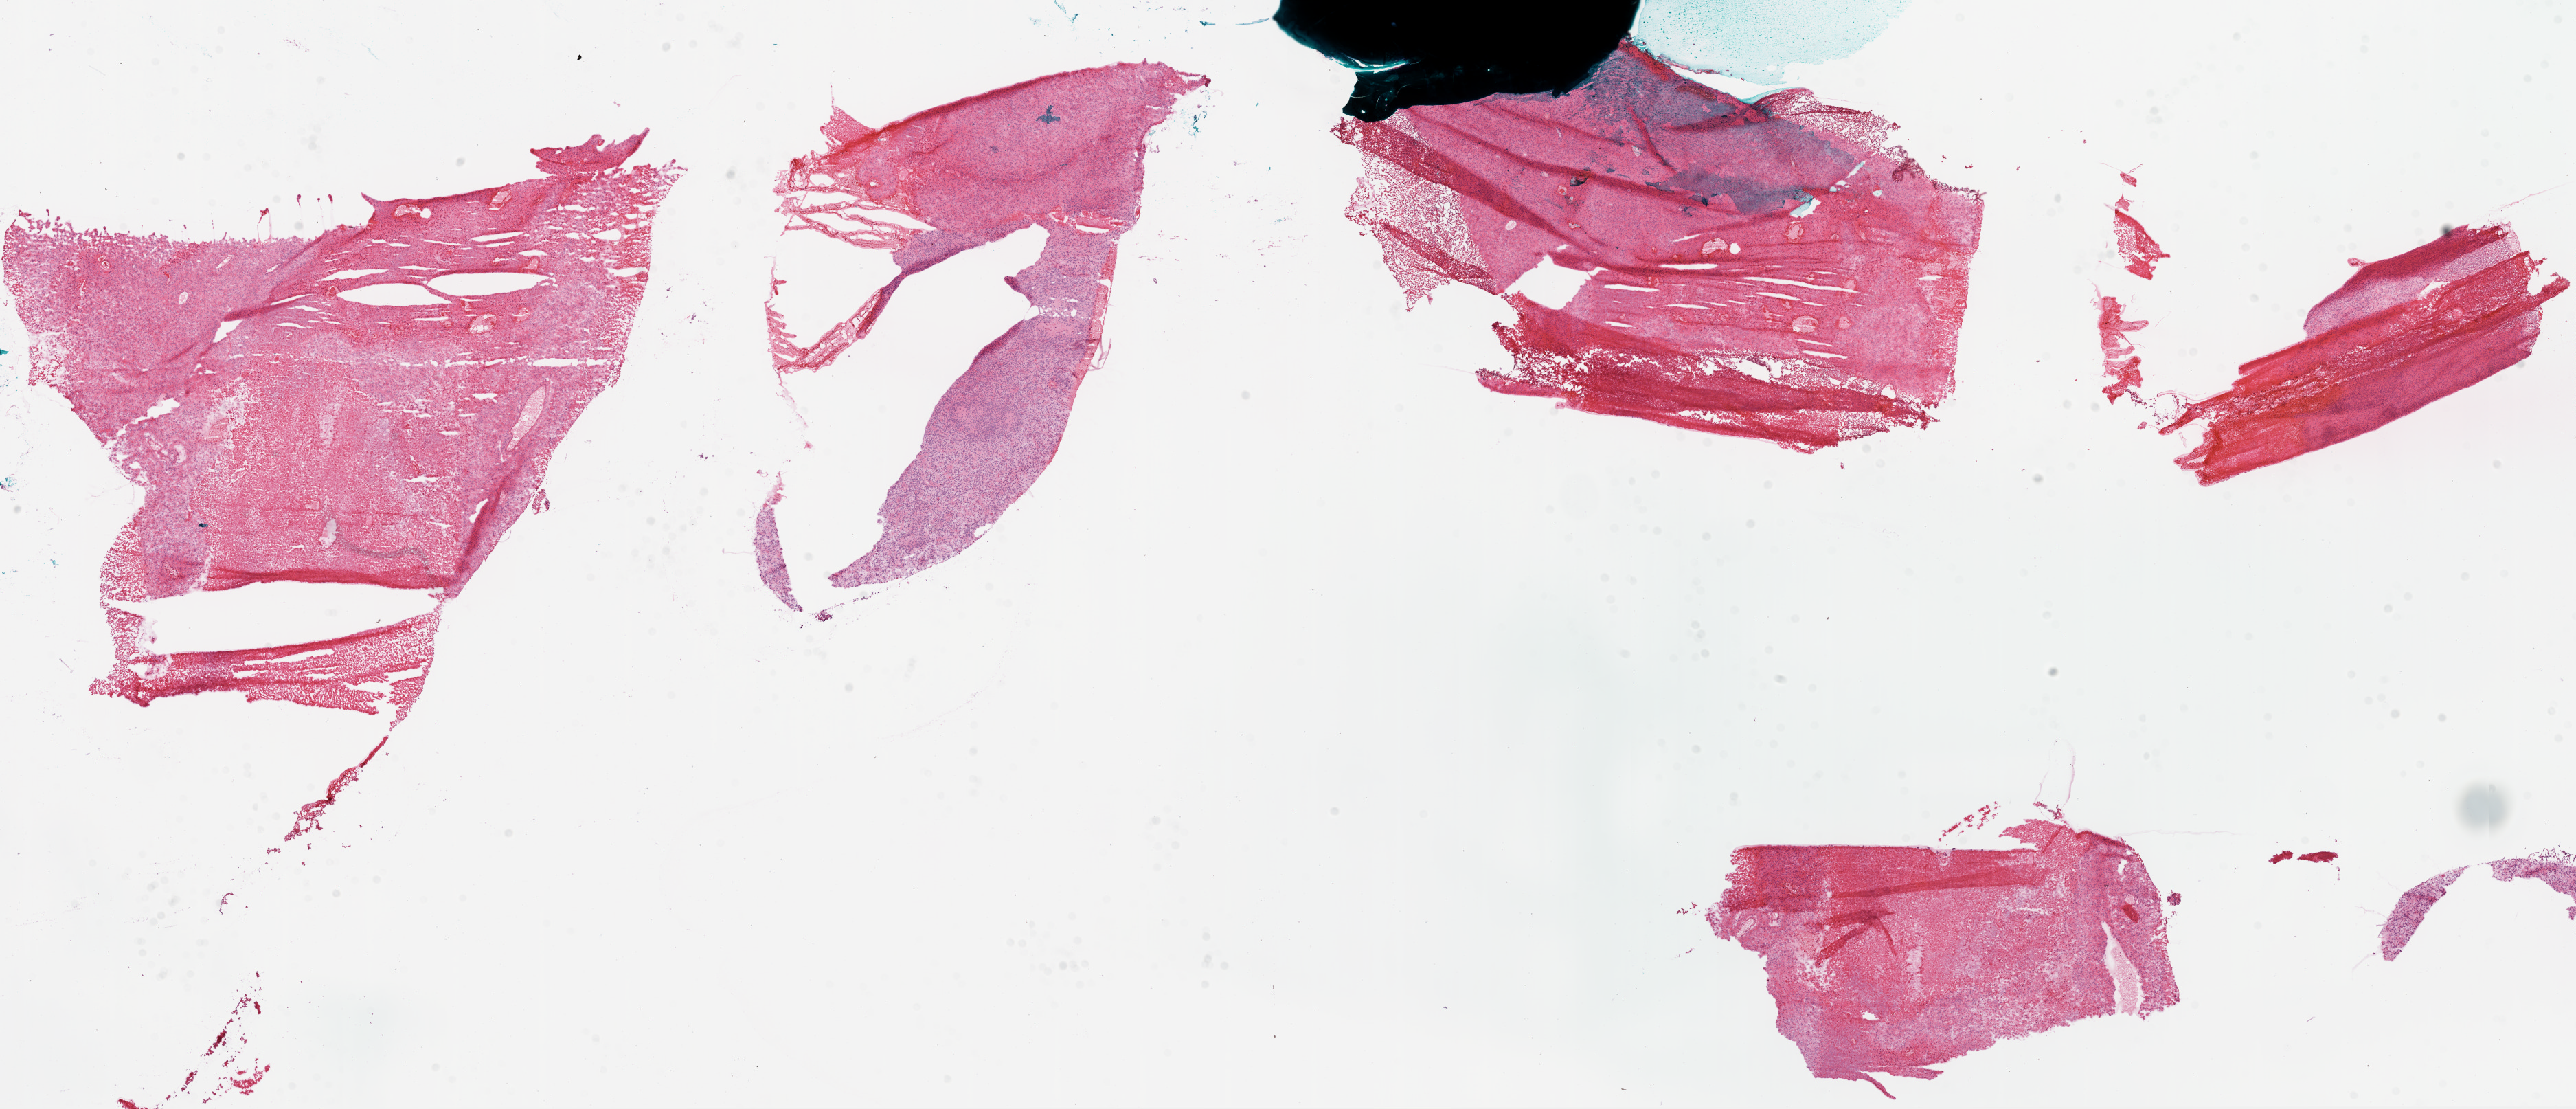
Hematoxylin and eosin (H&E) stained whole-slide image, a low-resolution overview of the entire scanned area, about 30.1 x 13.0 mm (from a 20x scan); frozen section from the bottom of the tissue portion; brain, primary tumour sample. Female, age 63 years at initial diagnosis. Composition of this section per pathologist review: tumour cells 75%, tumour nuclei 100%, normal cells 0%, stromal cells 0%, necrosis 25%.
Diagnosis: Glioblastoma.